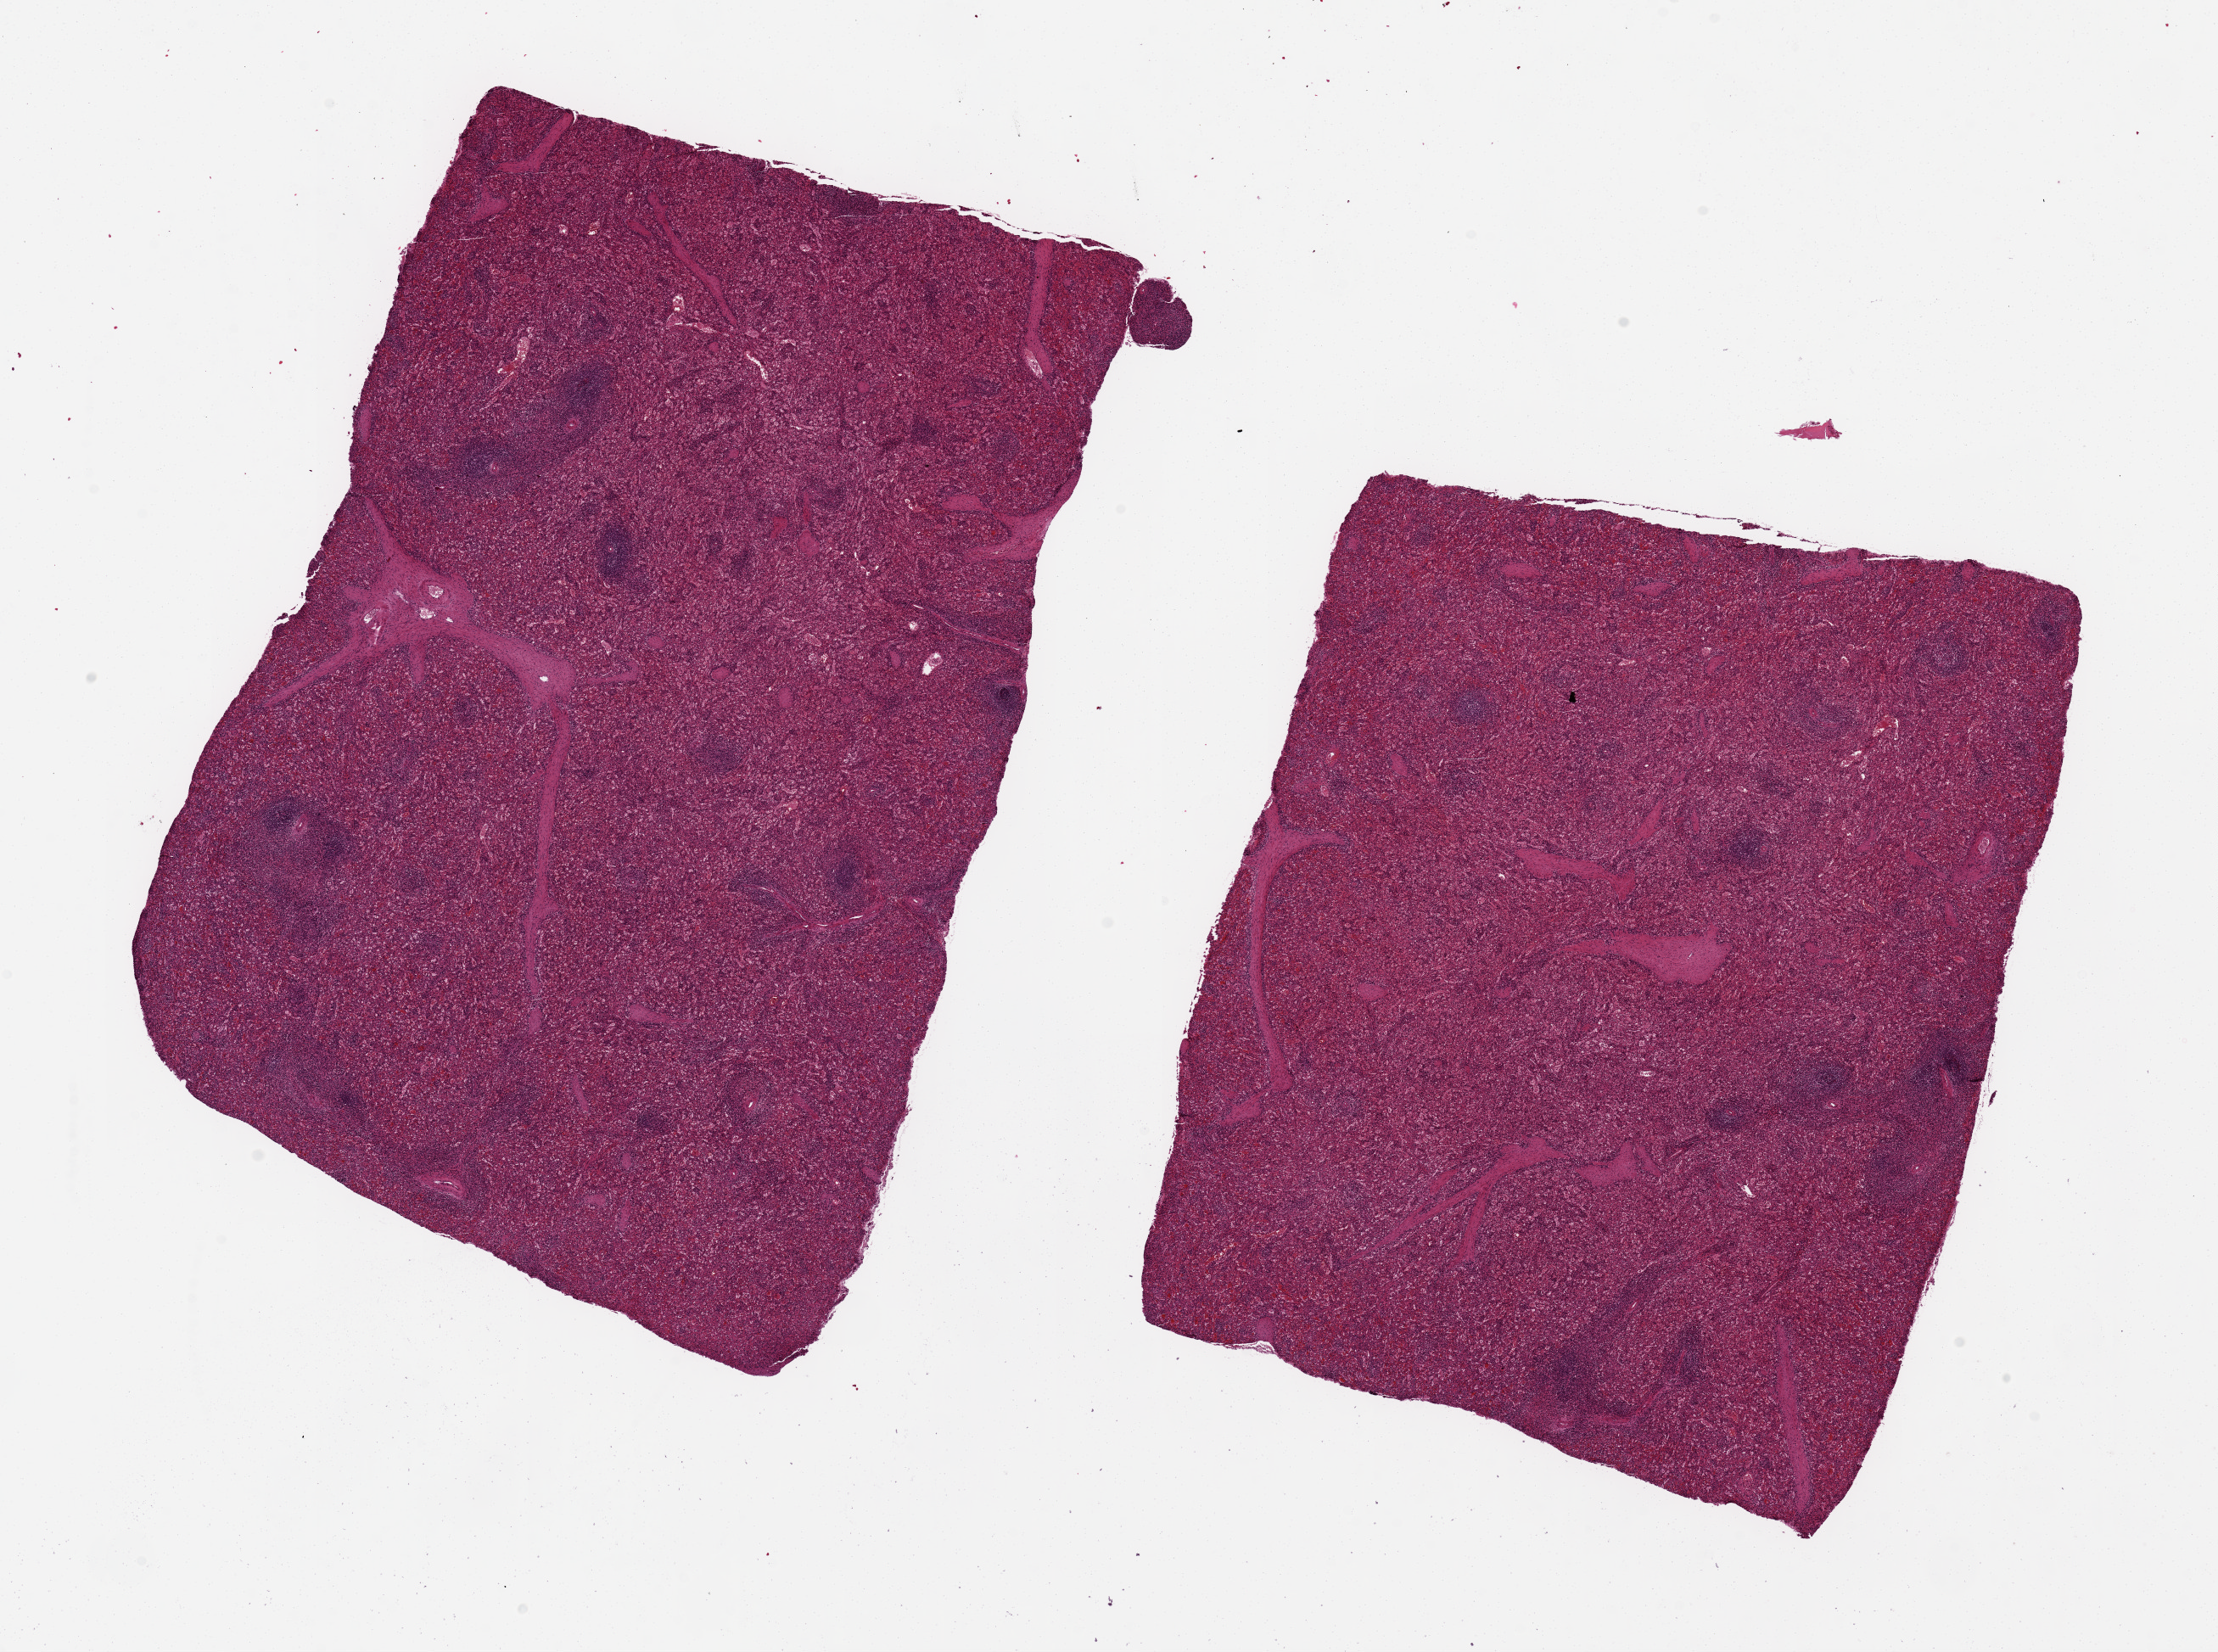
Digitized haematoxylin and eosin-stained section, whole scanned area (about 20.7 x 15.4 mm) shown as a low-resolution overview, PAXgene-fixed paraffin-embedded (PFPE) section, sampled site (target tissue): spleen, donor tissue sample. Donor sex: female.
- reviewer comment on this tissue sample: 2 ~8.5x7.5mm aliquots